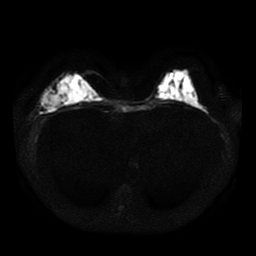
Breast MRI, one axial slice; slice 15 of 41 in the series (ordered by position); diffusion-weighted series; image 2 of 4 stored at this slice position (different b-values; order by instance number); 1.5 T; 256 × 256 image matrix, field of view 330 × 330 mm. Female patient.
Annotated regions visible in this slice (expert manual segmentation):
- tumour on diffusion-weighted imaging: bounding box <41,84,67,110> (left, top, right, bottom; pixels)